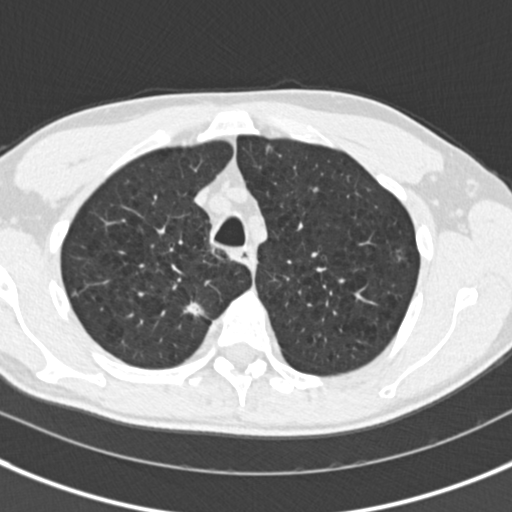
Low-dose screening chest CT, one axial slice. Slice 137 of 175 in the series (ordered by position). 120 kVp. Lung window (W 1500 / L -600 HU). 2 mm slice thickness. 512 × 512 image matrix, field of view 306 × 306 mm.
Annotated regions visible in this slice (manually delineated by an expert):
- lesion 2 (tumor, upper lobe of right lung): bounding box [x1, y1, x2, y2] px = [184, 301, 203, 316]